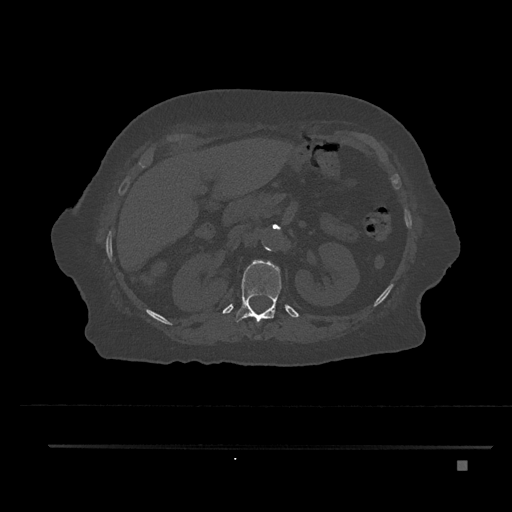
CT including the spine, one axial slice; reconstruction kernel Br40s/3; bone window (W 1800 / L 400 HU); 0.5 mm slice thickness; 512 × 512 image matrix. Female patient, age 76 years. From the clinical record (not read from this slice): primary cancer: lung; vertebrae with lytic lesions (as recorded): T11, L3.
Structures marked on this image (semi-automatically segmented with operator editing):
- T12 vertebra: bounding box <235,260,281,338> (left, top, right, bottom; pixels)